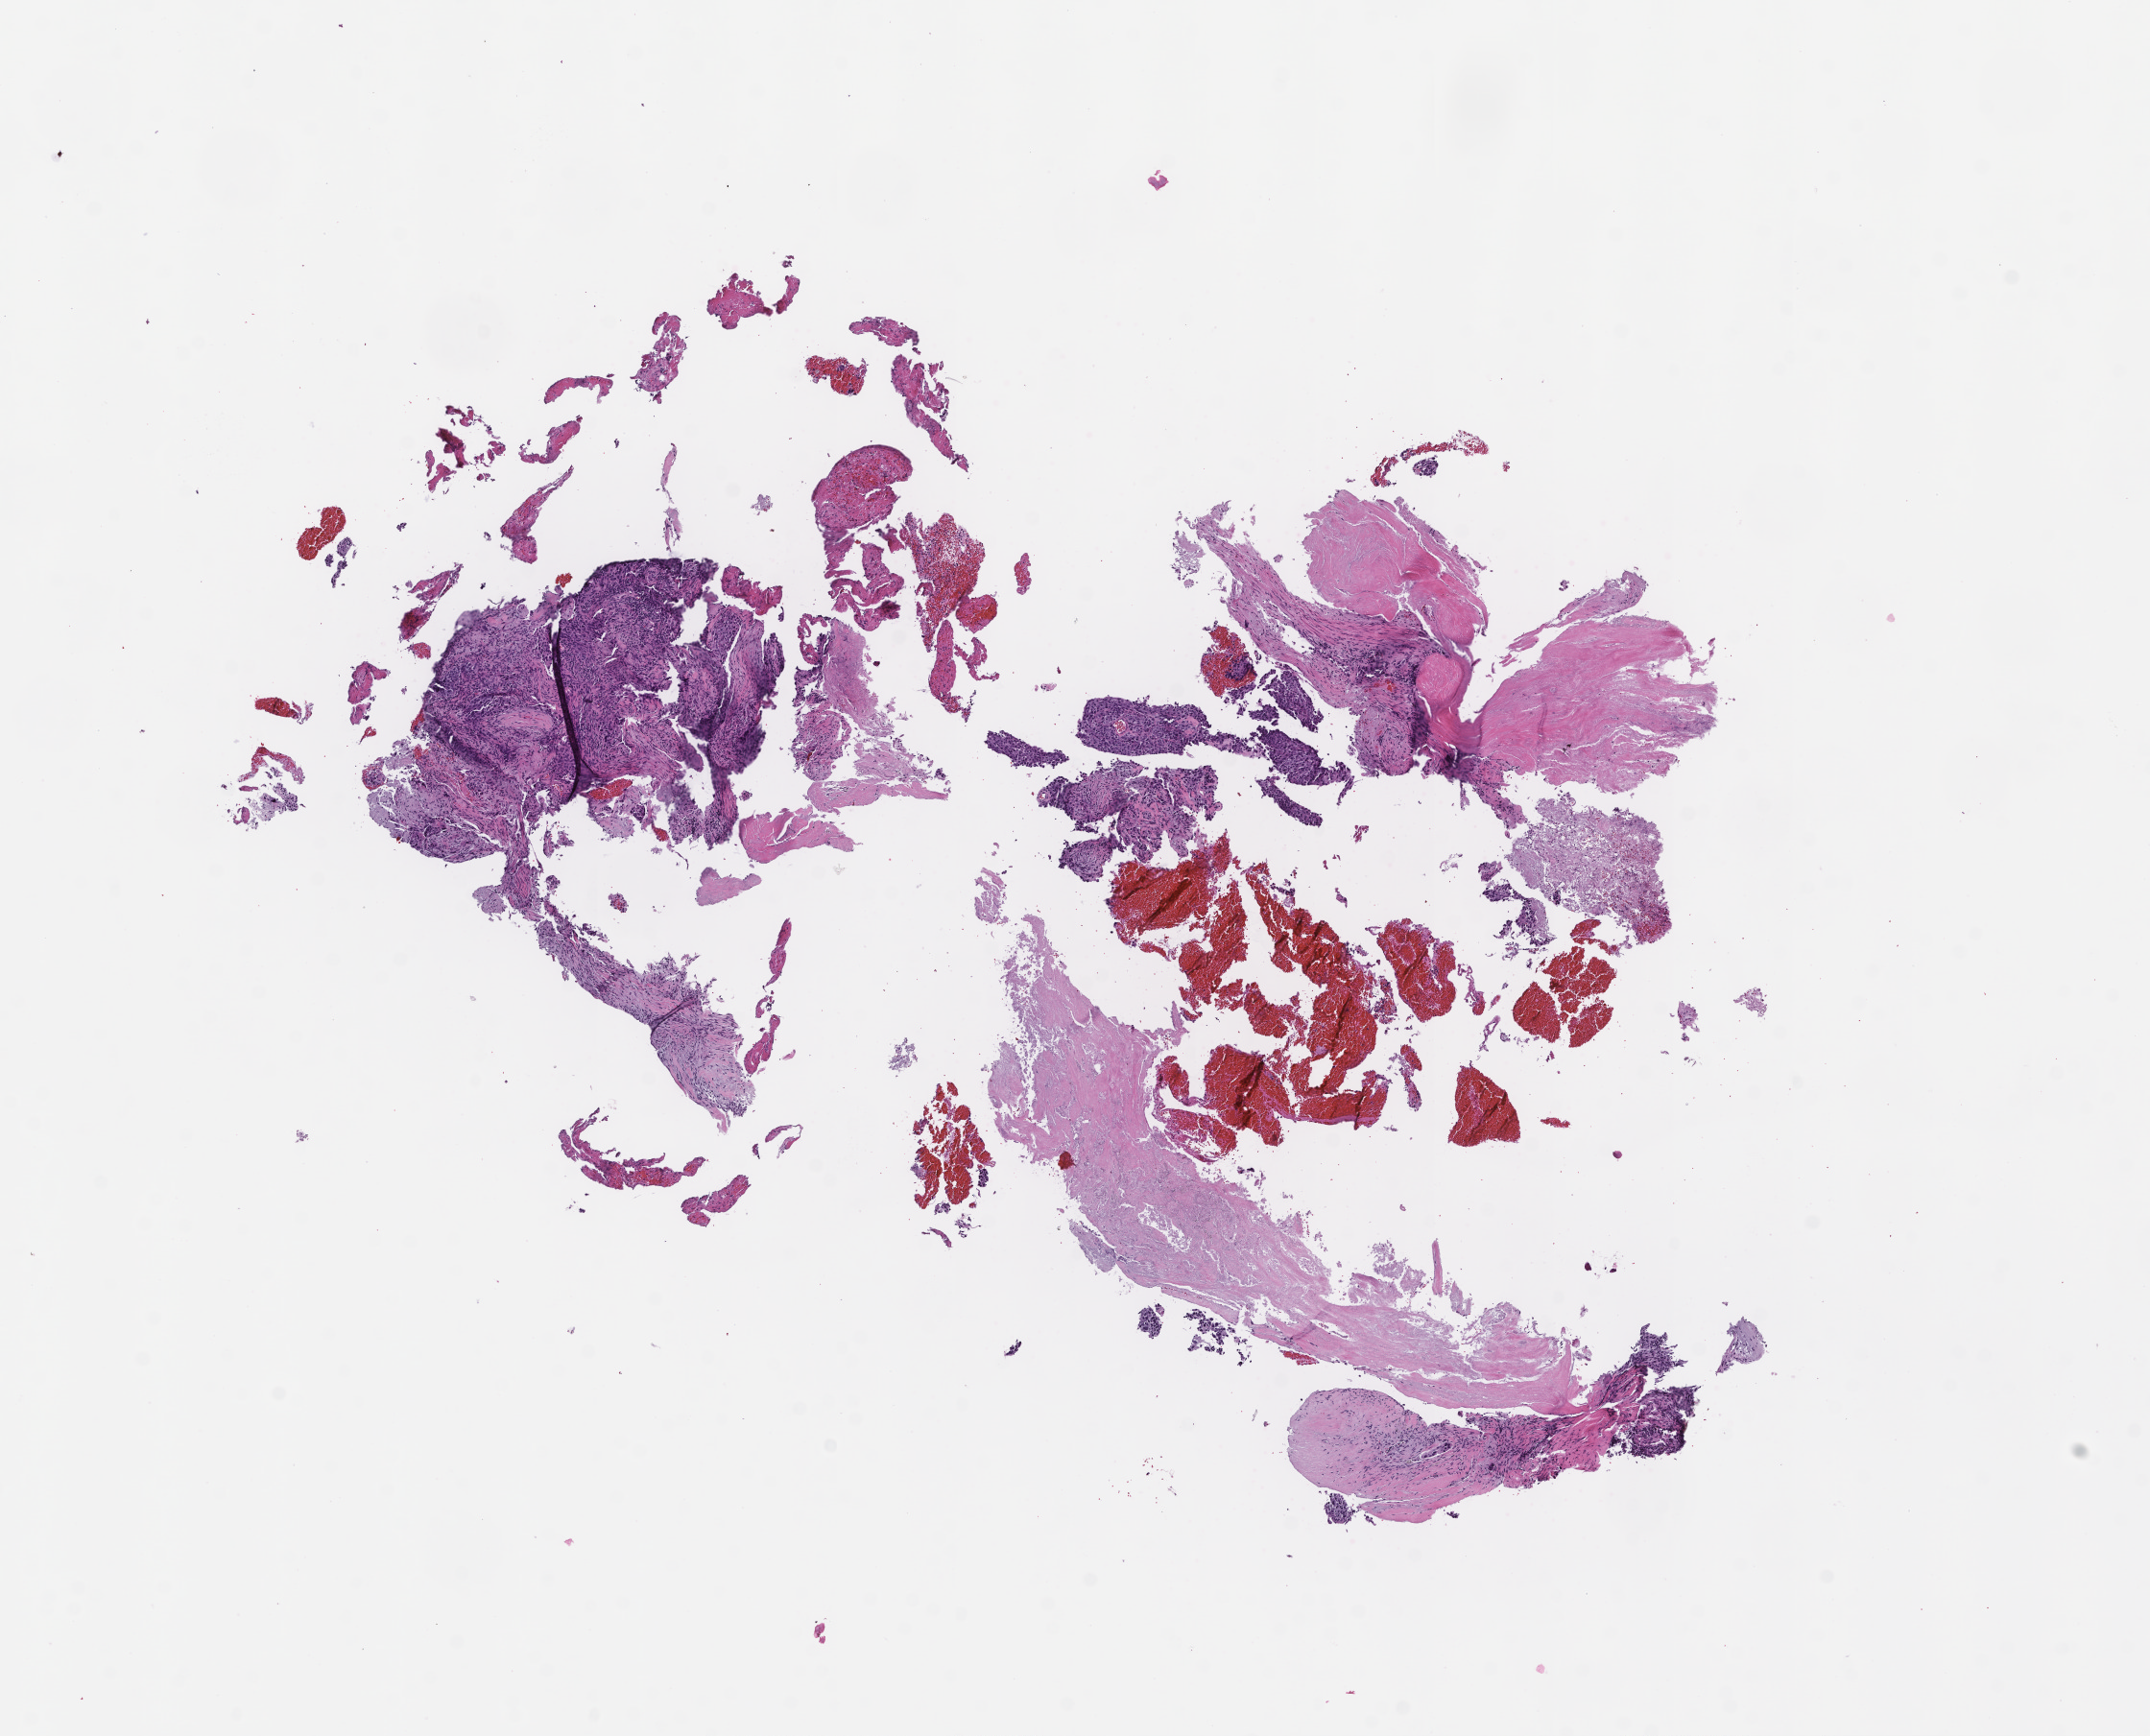
Digitized haematoxylin and eosin-stained section — whole scanned area (about 9.0 x 7.3 mm) shown as a low-resolution overview, formalin-fixed paraffin-embedded section, tissue site: lung, specimen time point: archival tissue. Patient: male.
This section: primary tumour tissue. Diagnosis: Non-Small Cell Lung Carcinoma.